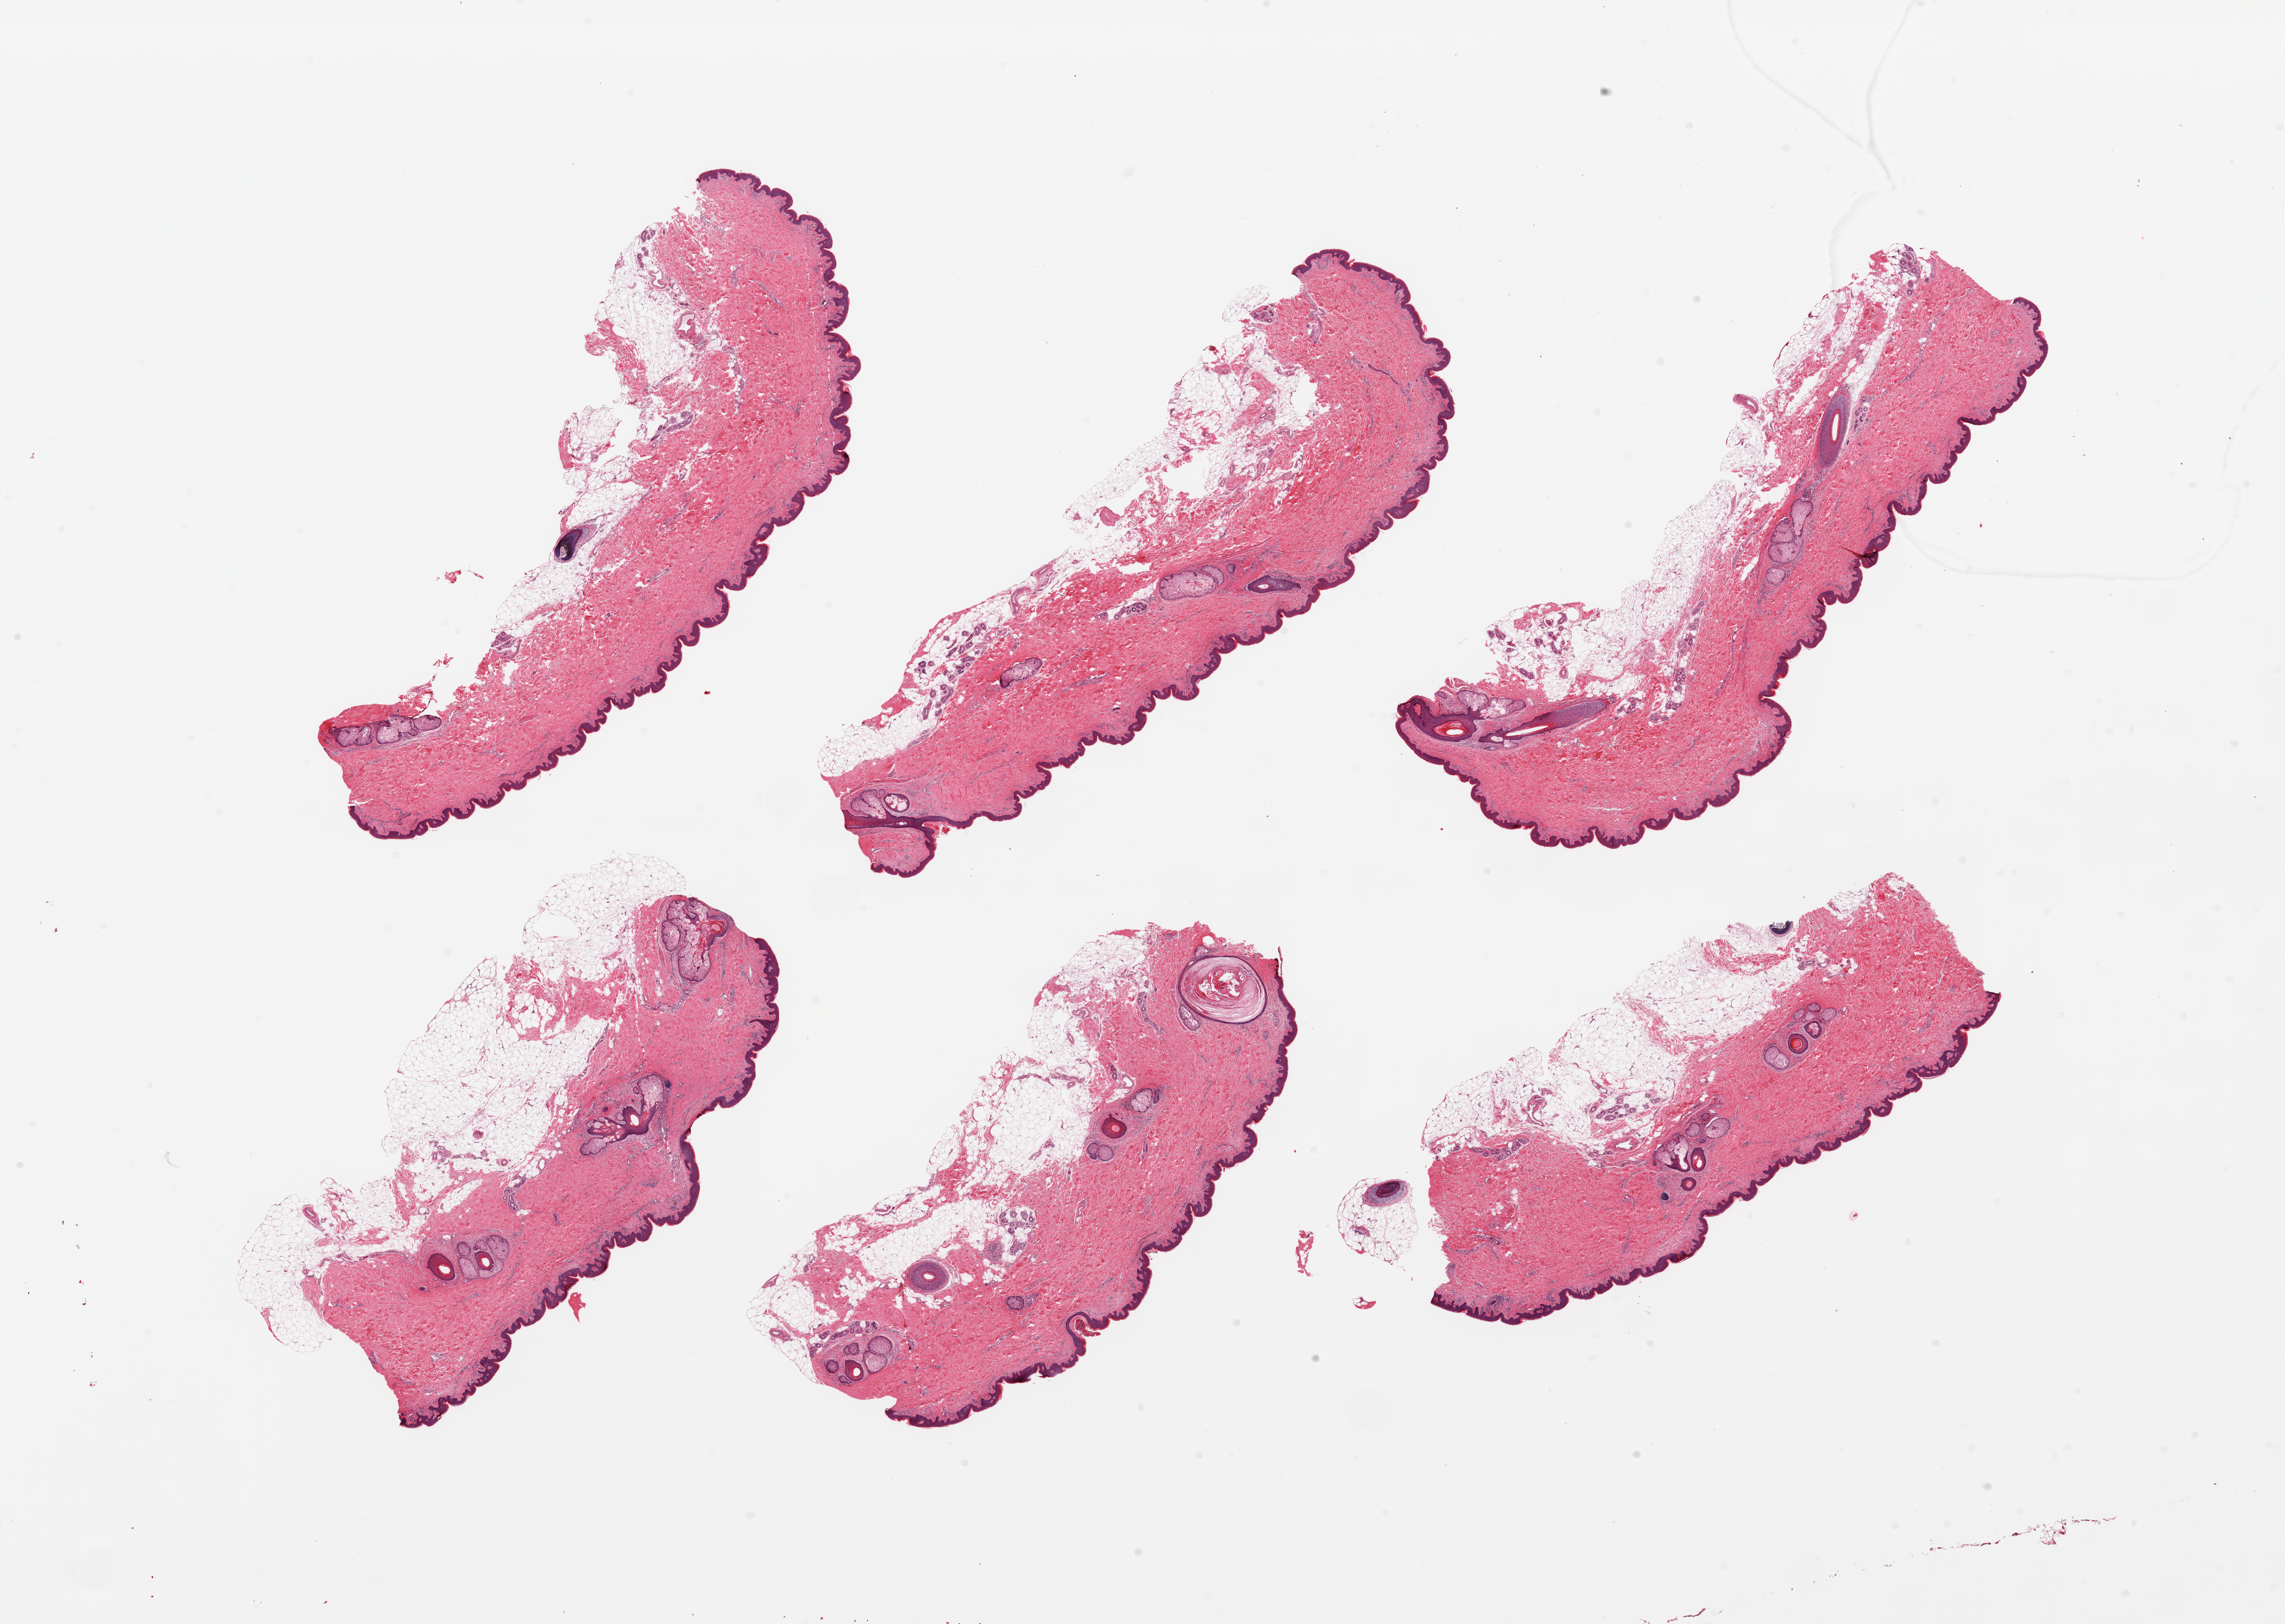
Digitized H&E-stained section — low-resolution overview of the scanned area, about 29.5 x 21.0 mm (slide scanned at 20x). PAXgene-fixed, paraffin-embedded tissue. Target tissue: skin of suprapubic region. Tissue donor sample. Donor sex: male.
Pathologist's review note for this sample: 6 pieces, adherent dermal fat up to ~2mm; squamous epithelium is ~70 microns.